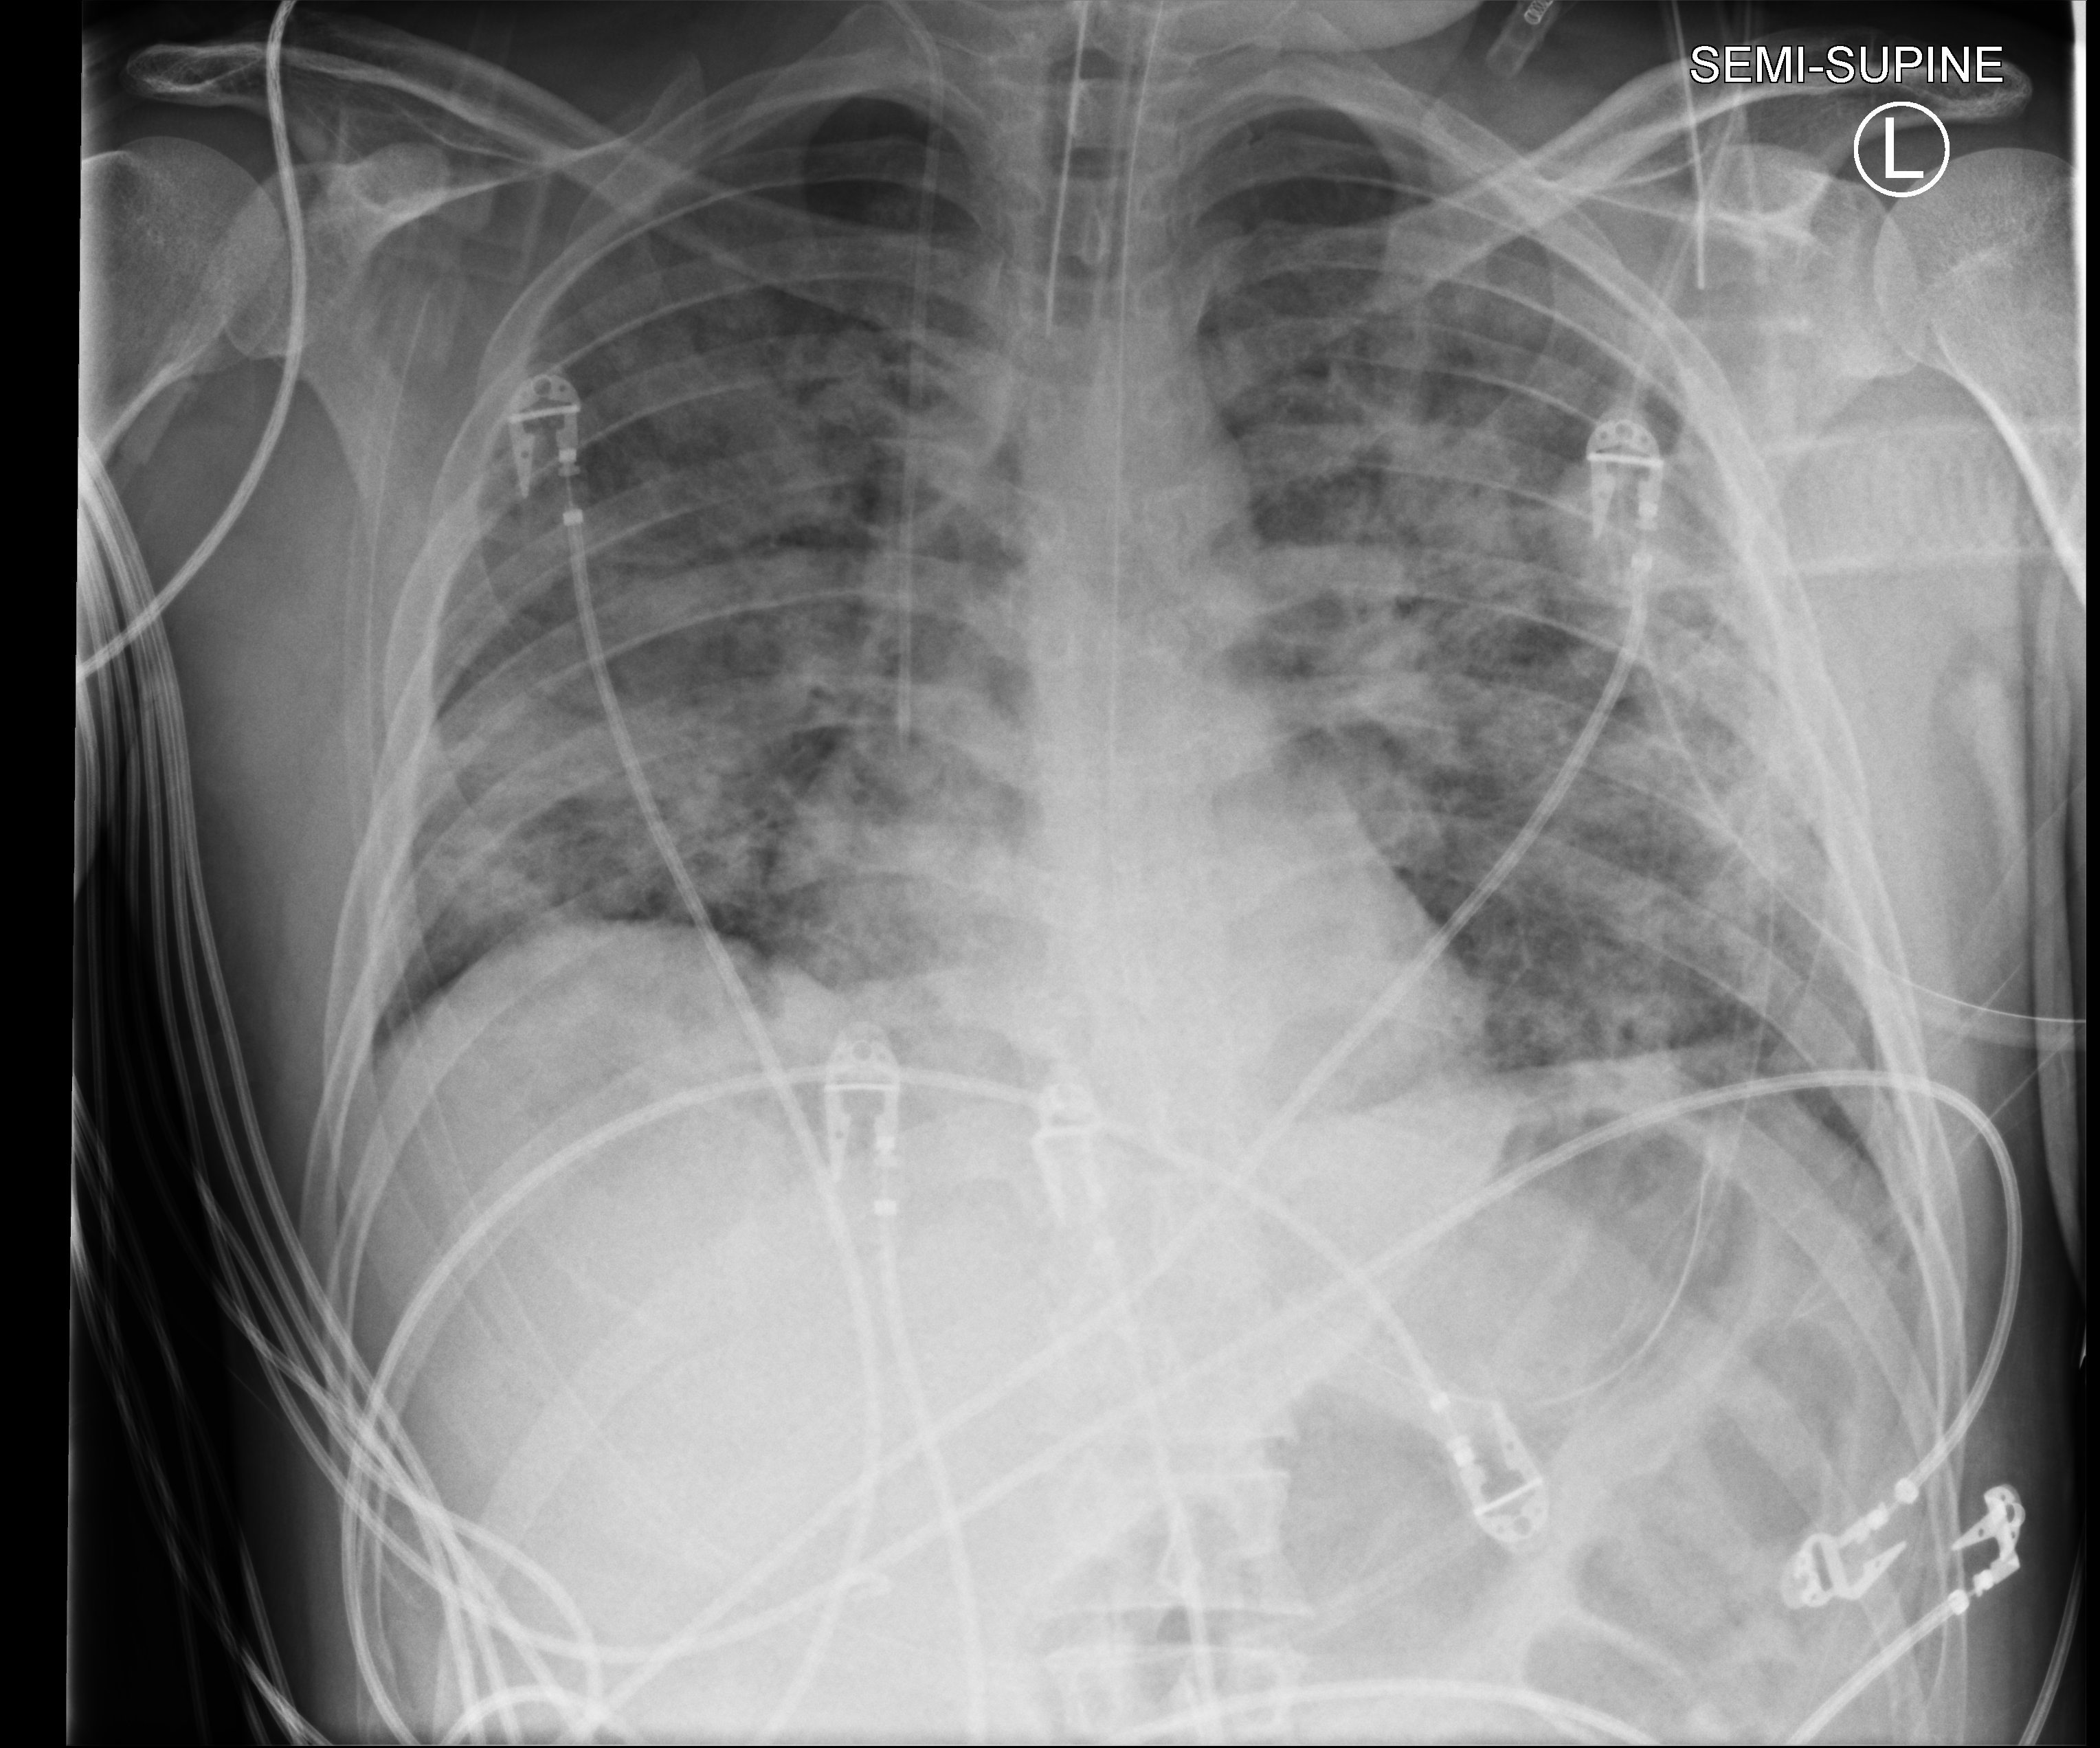
Bedside chest radiograph (computed radiography), anteroposterior (AP) projection. Patient hospitalised with COVID-19; male, aged 18–59 years.
Admission-level facts for this patient (not findings on this image; timing relative to this image not recorded): mechanically ventilated during this hospital stay: yes; admitted to intensive care during this hospital stay: yes.